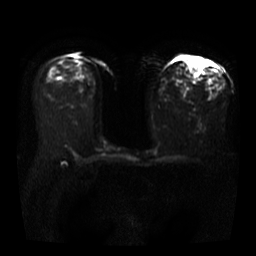
Breast MRI, one axial slice. Position 21 of 40 along the scan axis. Diffusion-weighted series; image 2 of 4 stored at this slice position (different b-values; order by instance number). 3 T. 5 mm slice thickness. 256 × 256 image matrix, field of view 360 × 360 mm. Female patient.
Outlined on this slice (manually delineated by an expert):
- tumour on diffusion-weighted imaging: bounding box [x1, y1, x2, y2] px = [187, 58, 199, 76]